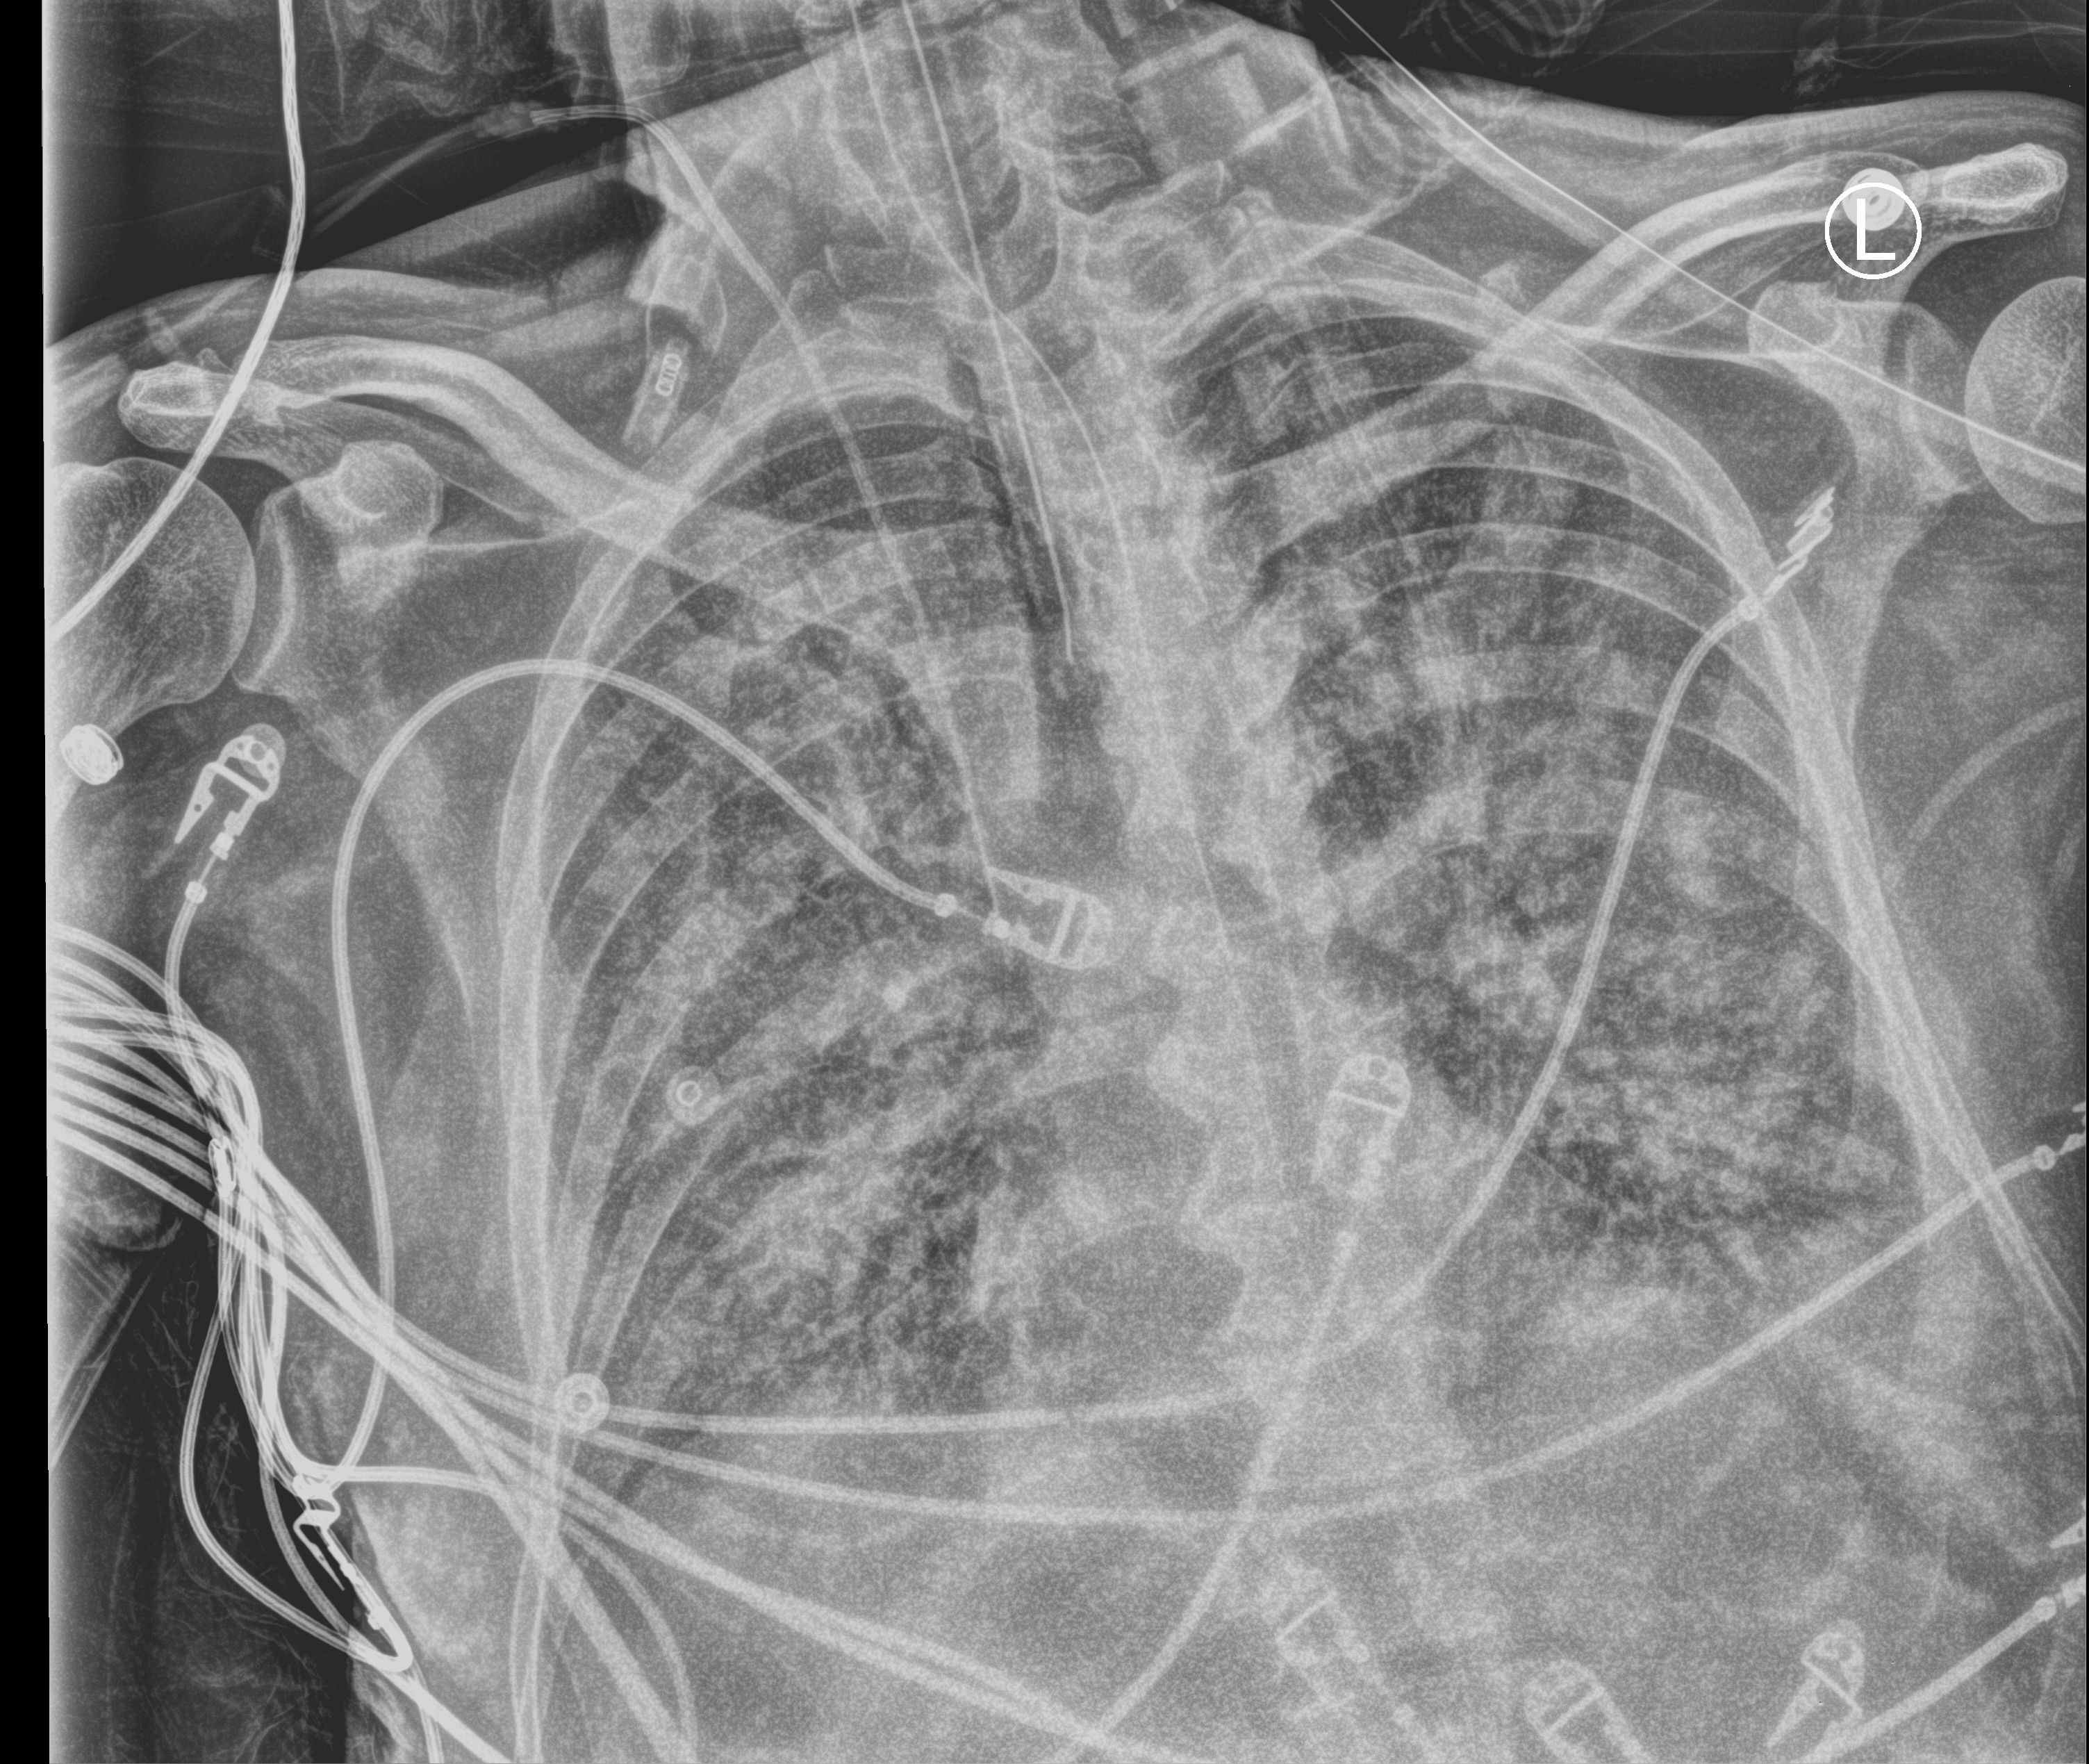
Portable chest radiograph. Patient hospitalised with COVID-19; male, aged 60–74 years.
From the hospital-stay record, not from the radiograph (when in the stay this image was taken is not recorded): admitted to intensive care during this hospital stay: yes; smoking status (admission record): never.